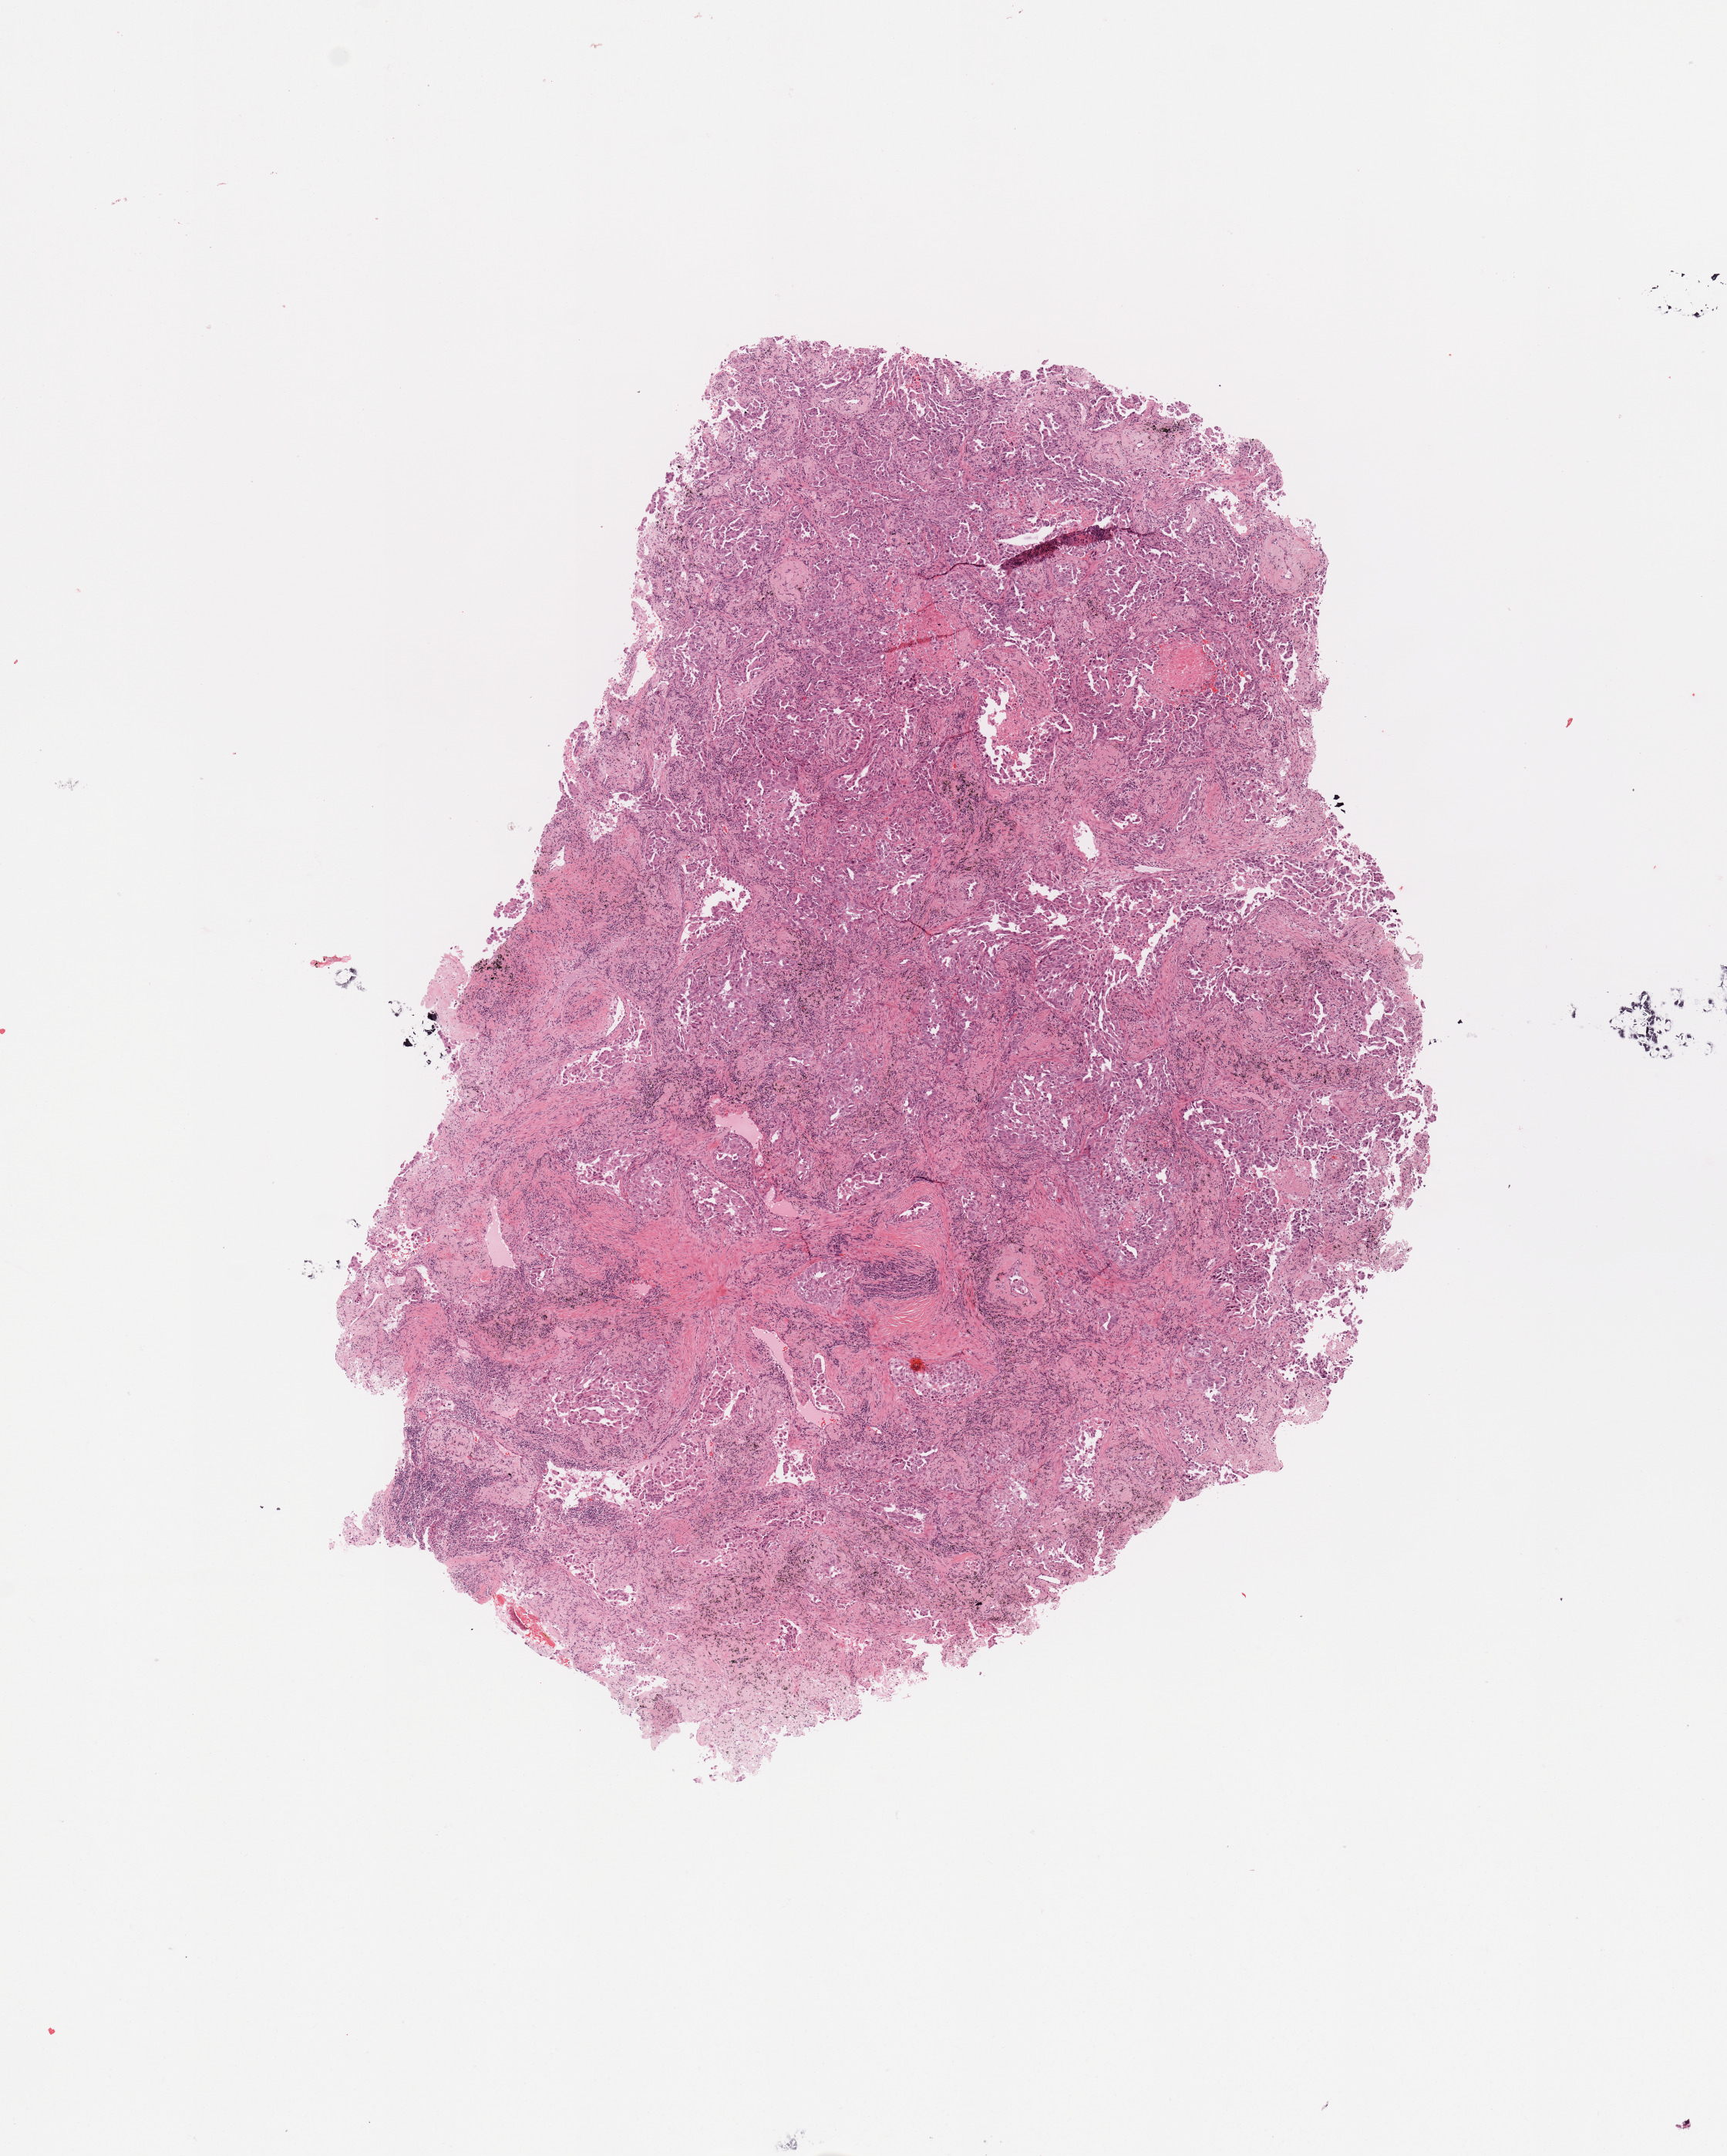
Digitized H&E tissue section (whole slide) — shown as a low-resolution overview of the whole scanned area (about 8.9 x 11.1 mm, acquisition: 20x scan); tumour tissue sample, sampled site: lung. Patient: female, age 79 years. Histologic grade: G3 (poorly differentiated). Pathologist review of this section (percent, as recorded): tumour nuclei 75%, necrosis 3%.
Histologic diagnosis: Adenocarcinoma, NOS. AJCC pathologic stage: IIA. Primary tumour site (as recorded): right middle lobe.